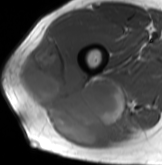
MRI of an extremity soft-tissue mass, one axial slice; slice 56 of 61 in the series (ordered by position); MR volume resampled by the dataset authors to the PET/CT grid (not the native acquisition matrix); 3.27 mm slice thickness; 162 × 165 image matrix. Male patient. Case-level facts recorded for this patient, not image findings: histological type: poorly differentiated synovial sarcoma; grade: high; site of the primary tumour: right buttock.
Annotated regions visible in this slice (expert contour drawn on MRI and transferred to this co-registered scan by the dataset authors):
- gross tumour volume including surrounding oedema: bounding box (x1, y1, x2, y2) in pixels: (16, 34, 138, 146)
- gross tumour volume (mass): (16, 34, 124, 146)